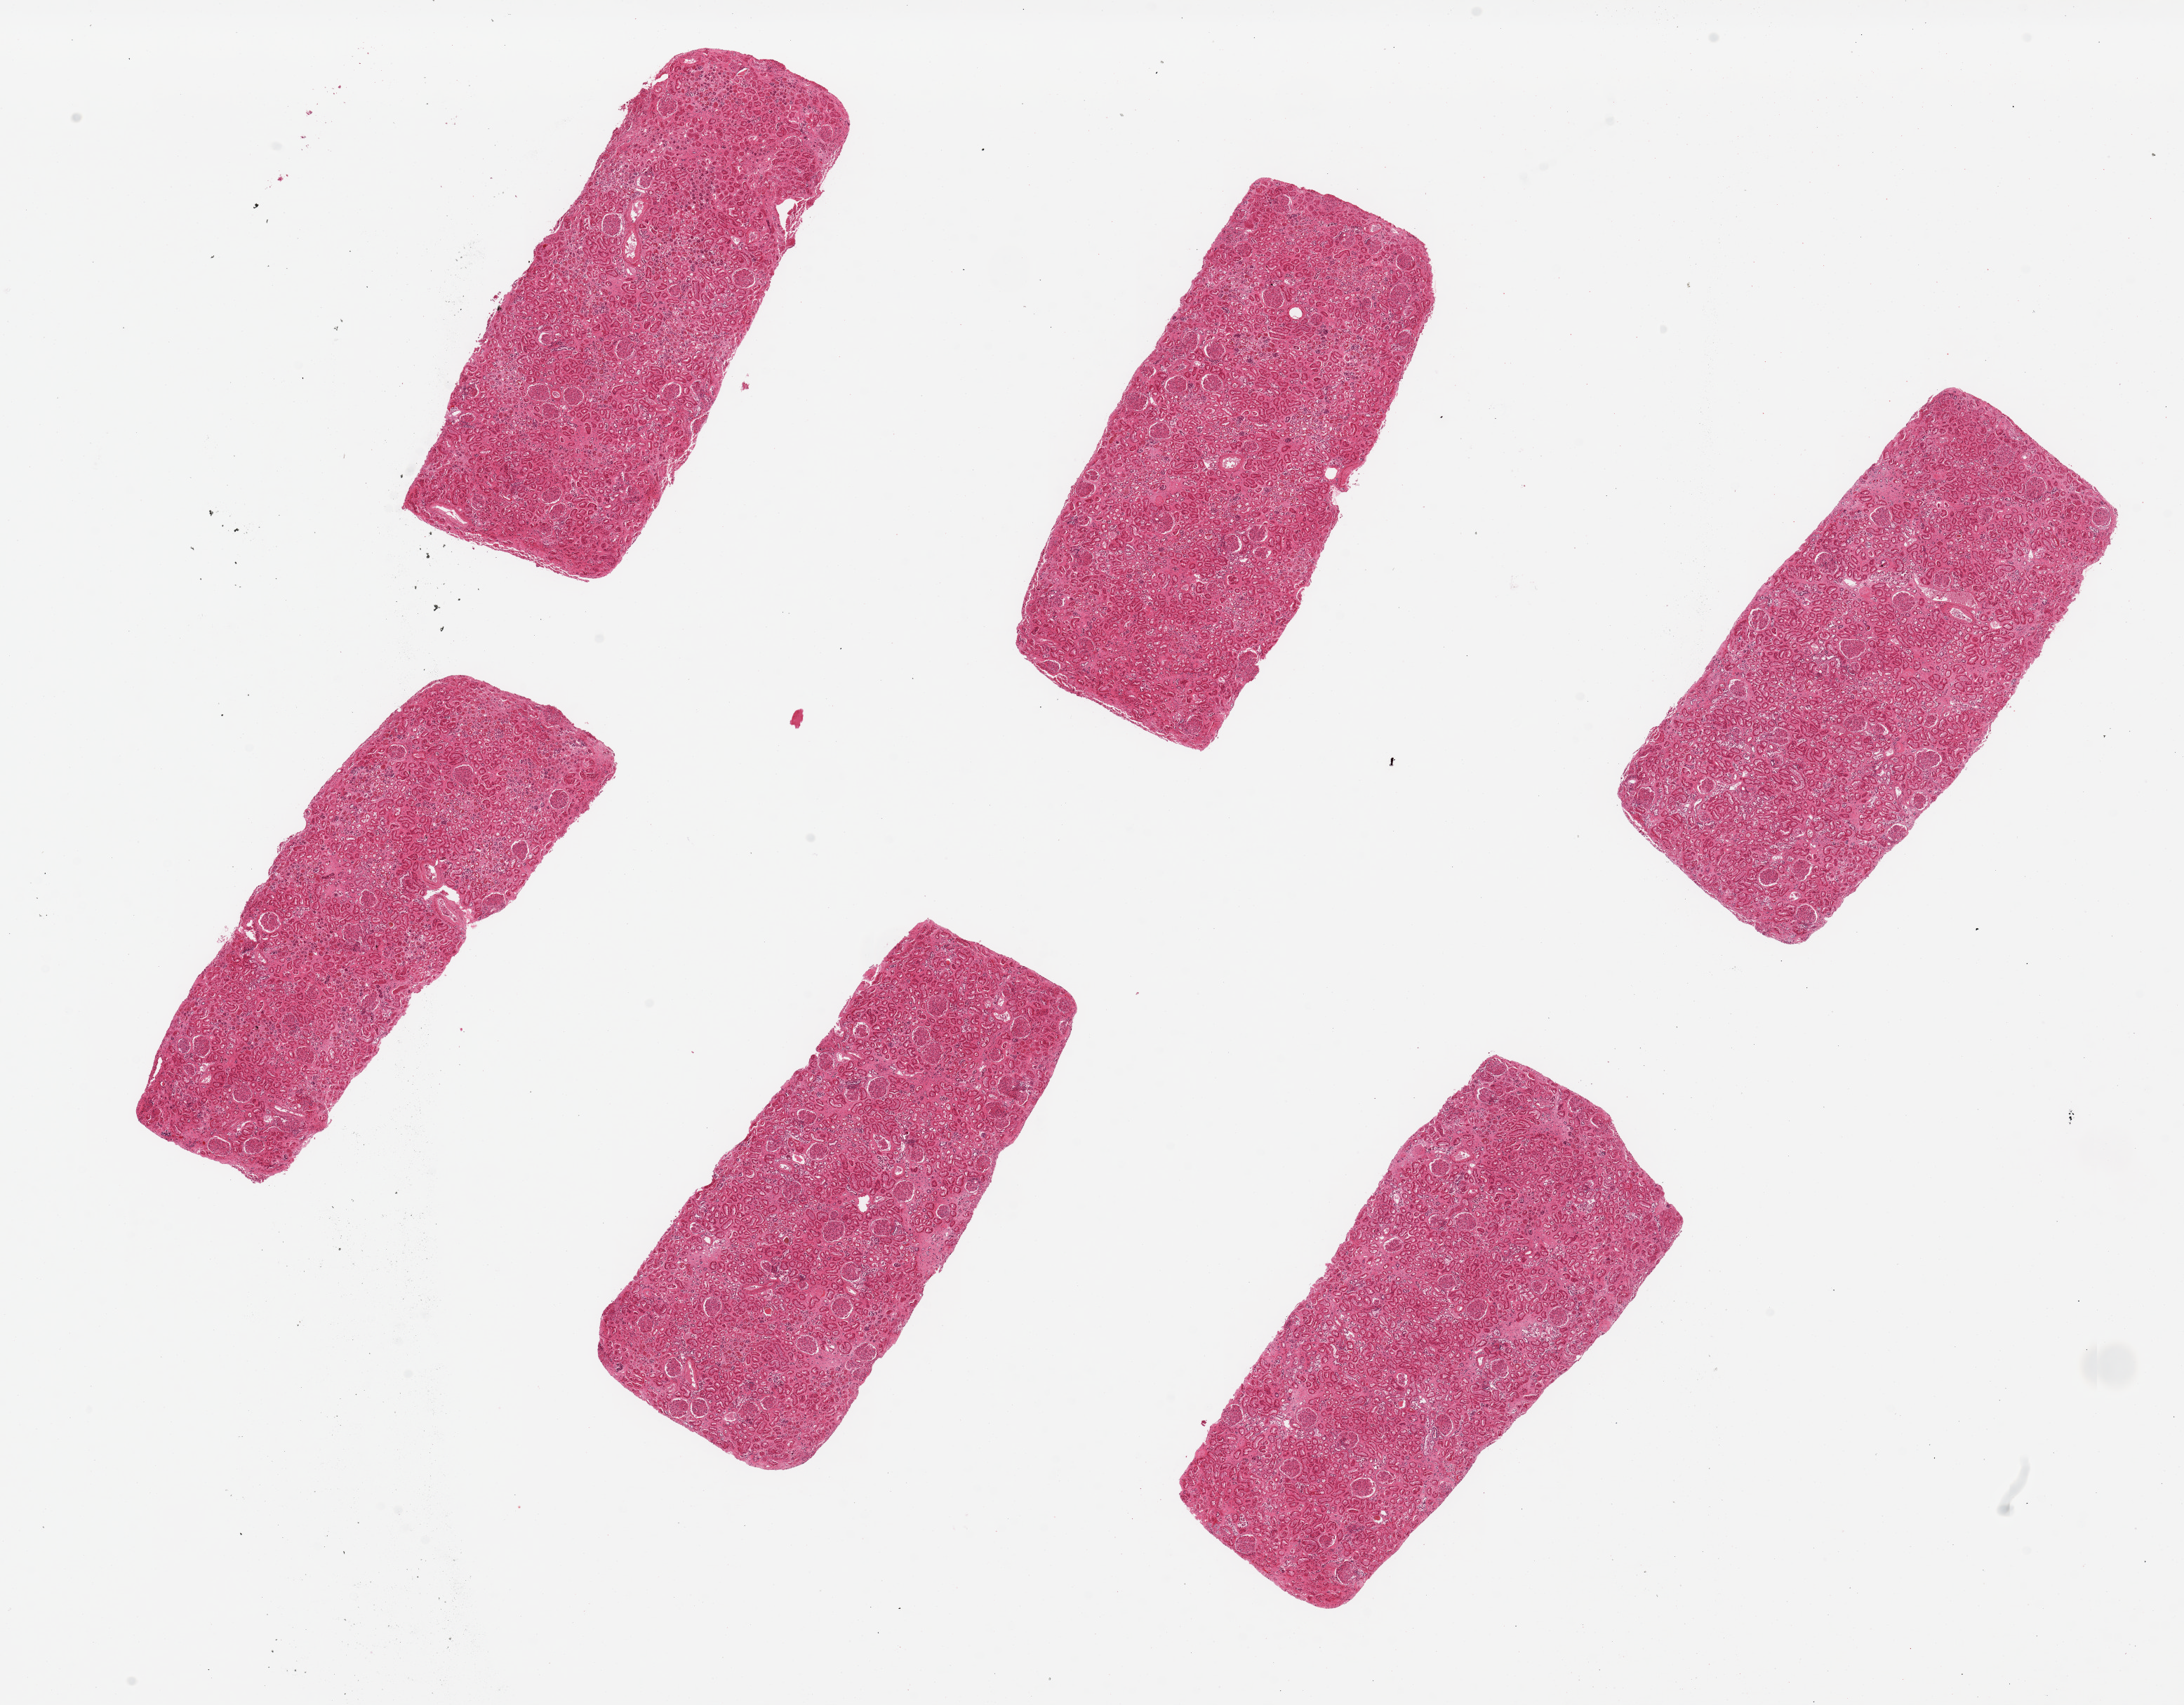
Whole-slide image, H&E stain — low-resolution overview of the scanned area, about 24.6 x 19.2 mm (from a 20x scan); PAXgene-fixed, paraffin-embedded tissue; sampled site (target tissue): renal cortex; tissue donor sample. Donor sex: male.
Pathologist's review note for this sample: 6 pieces, ~6.5x2.5mm . Tublules moderately--severely autolyzed.